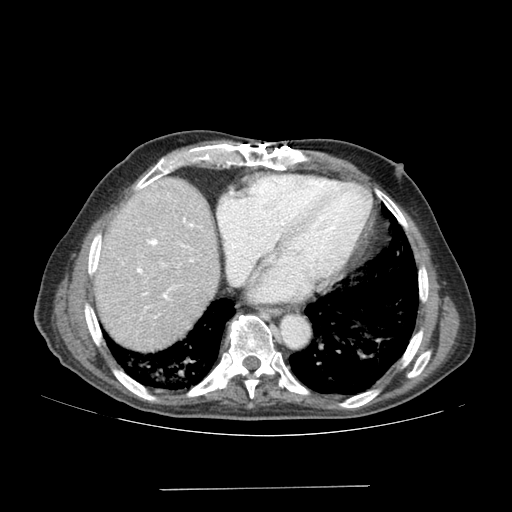
Contrast-enhanced abdominal CT (liver protocol), one axial slice. Slice 154 of 192 in the series (ordered by position). 120 kVp. Soft-tissue window (W 400 / L 40 HU). 512 × 512 image matrix, field of view 400 × 400 mm. From the clinical record (not read from this slice): diagnosis: hepatocellular carcinoma (patient treated with transarterial chemoembolisation; whether this scan precedes or follows treatment is not stated here); TNM stage (as recorded): Stage-IVA; Child-Pugh class: A; tumour nodularity: uninodular.
Annotated regions visible in this slice (semi-automatically segmented with operator editing):
- liver parenchyma outside the tumour (the mass and vessels are separate outlines, so this box may not span the whole liver): bounding box <94,178,218,350> (left, top, right, bottom; pixels)
- liver vessels: <137,218,193,299>